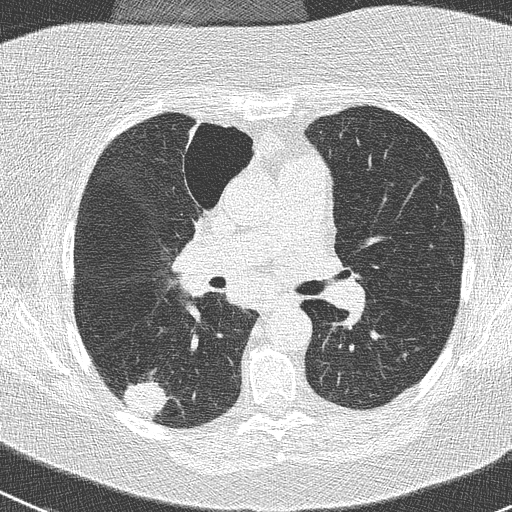
Axial slice from a low-dose chest CT screening exam; baseline annual screen; lung window (W 1500 / L -600 HU); 2 mm slice thickness; slice 112 of 261 in the series; 512 × 512 image matrix, field of view 310 × 310 mm. Female participant, aged 74 years at enrolment. Former smoker at enrolment.
Lesion marked by an expert reader, bounding box (x1, y1, x2, y2) in pixels: (117, 376, 173, 426). The screening reader recorded 3 non-calcified nodules or masses ≥4 mm on this exam; which of them this box marks is not recorded. Official screen result: positive, change unspecified: nodule(s) >= 4 mm or enlarging nodule(s), mass(es), or other non-specific abnormalities suspicious for lung cancer. Participant outcome: lung cancer diagnosed 16 days after this screen — non-small cell carcinoma, right lower lobe, poorly differentiated (G3), stage IIIA (AJCC 6th edition), 28 mm at pathology.